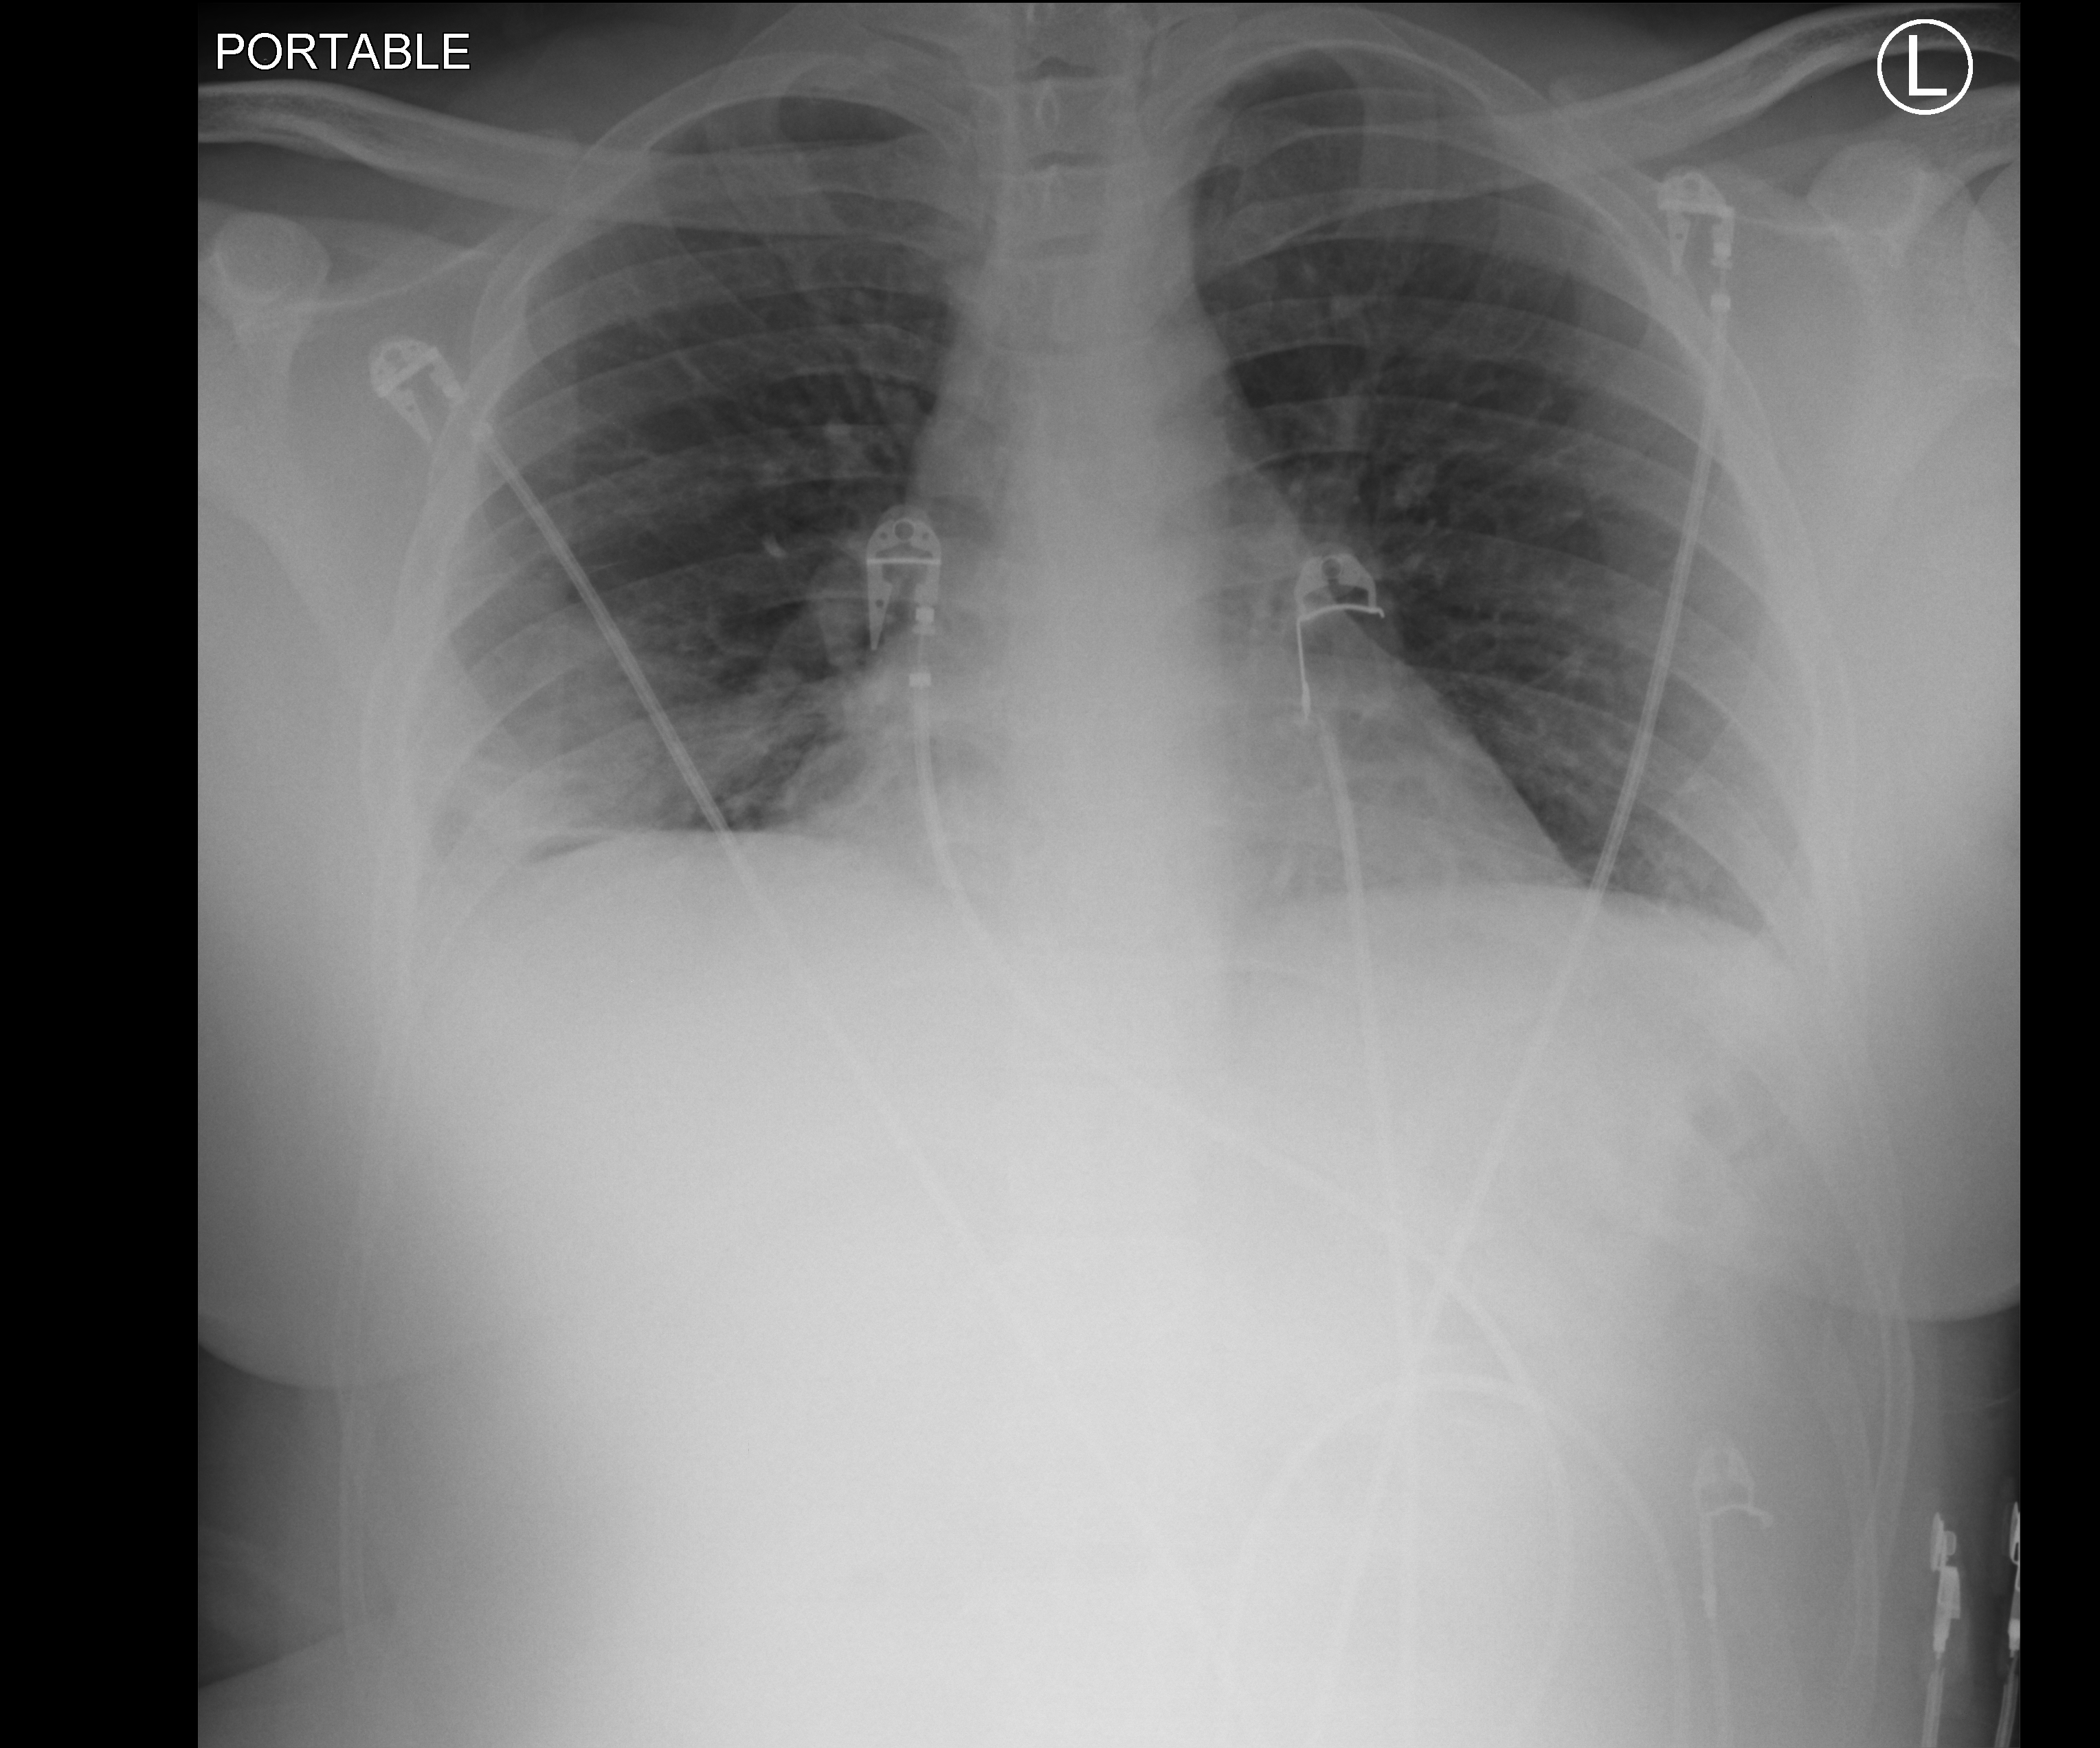
Bedside chest radiograph (computed radiography); anteroposterior (AP) projection. Male patient hospitalised with COVID-19, age 18–59 years.
From the hospital-stay record, not from the radiograph (when in the stay this image was taken is not recorded): mechanically ventilated during this hospital stay: no; admitted to intensive care during this hospital stay: no.